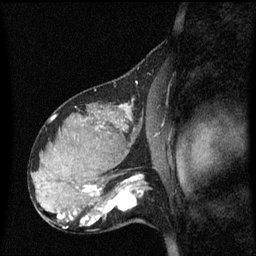
Breast MRI (dynamic contrast-enhanced), one sagittal slice; slice 36 of 60 in the series (ordered by position); dynamic contrast-enhanced series, image 2 of 3 at this slice position (ordered by acquisition); 1.5 T; TE 4.2 ms, TR 8.4 ms; 256 × 256 image matrix, field of view 210 × 210 mm. Female patient, age 31 years. Case-level facts recorded for this patient, not image findings: setting: breast cancer imaged before/during neoadjuvant chemotherapy; receptor status: HR-positive, HER2-negative.
Annotated regions visible in this slice (semi-automatic segmentation, software-assisted and operator-edited):
- analysis volume of interest (the breast-tissue region the enhancement analysis was run in; not a lesion): box from (x=98, y=175) to (x=153, y=228) px
- tumour enhancement mask (voxels above the 70 % enhancement threshold inside the analysis volume of interest): (x=98, y=176)–(x=144, y=220)